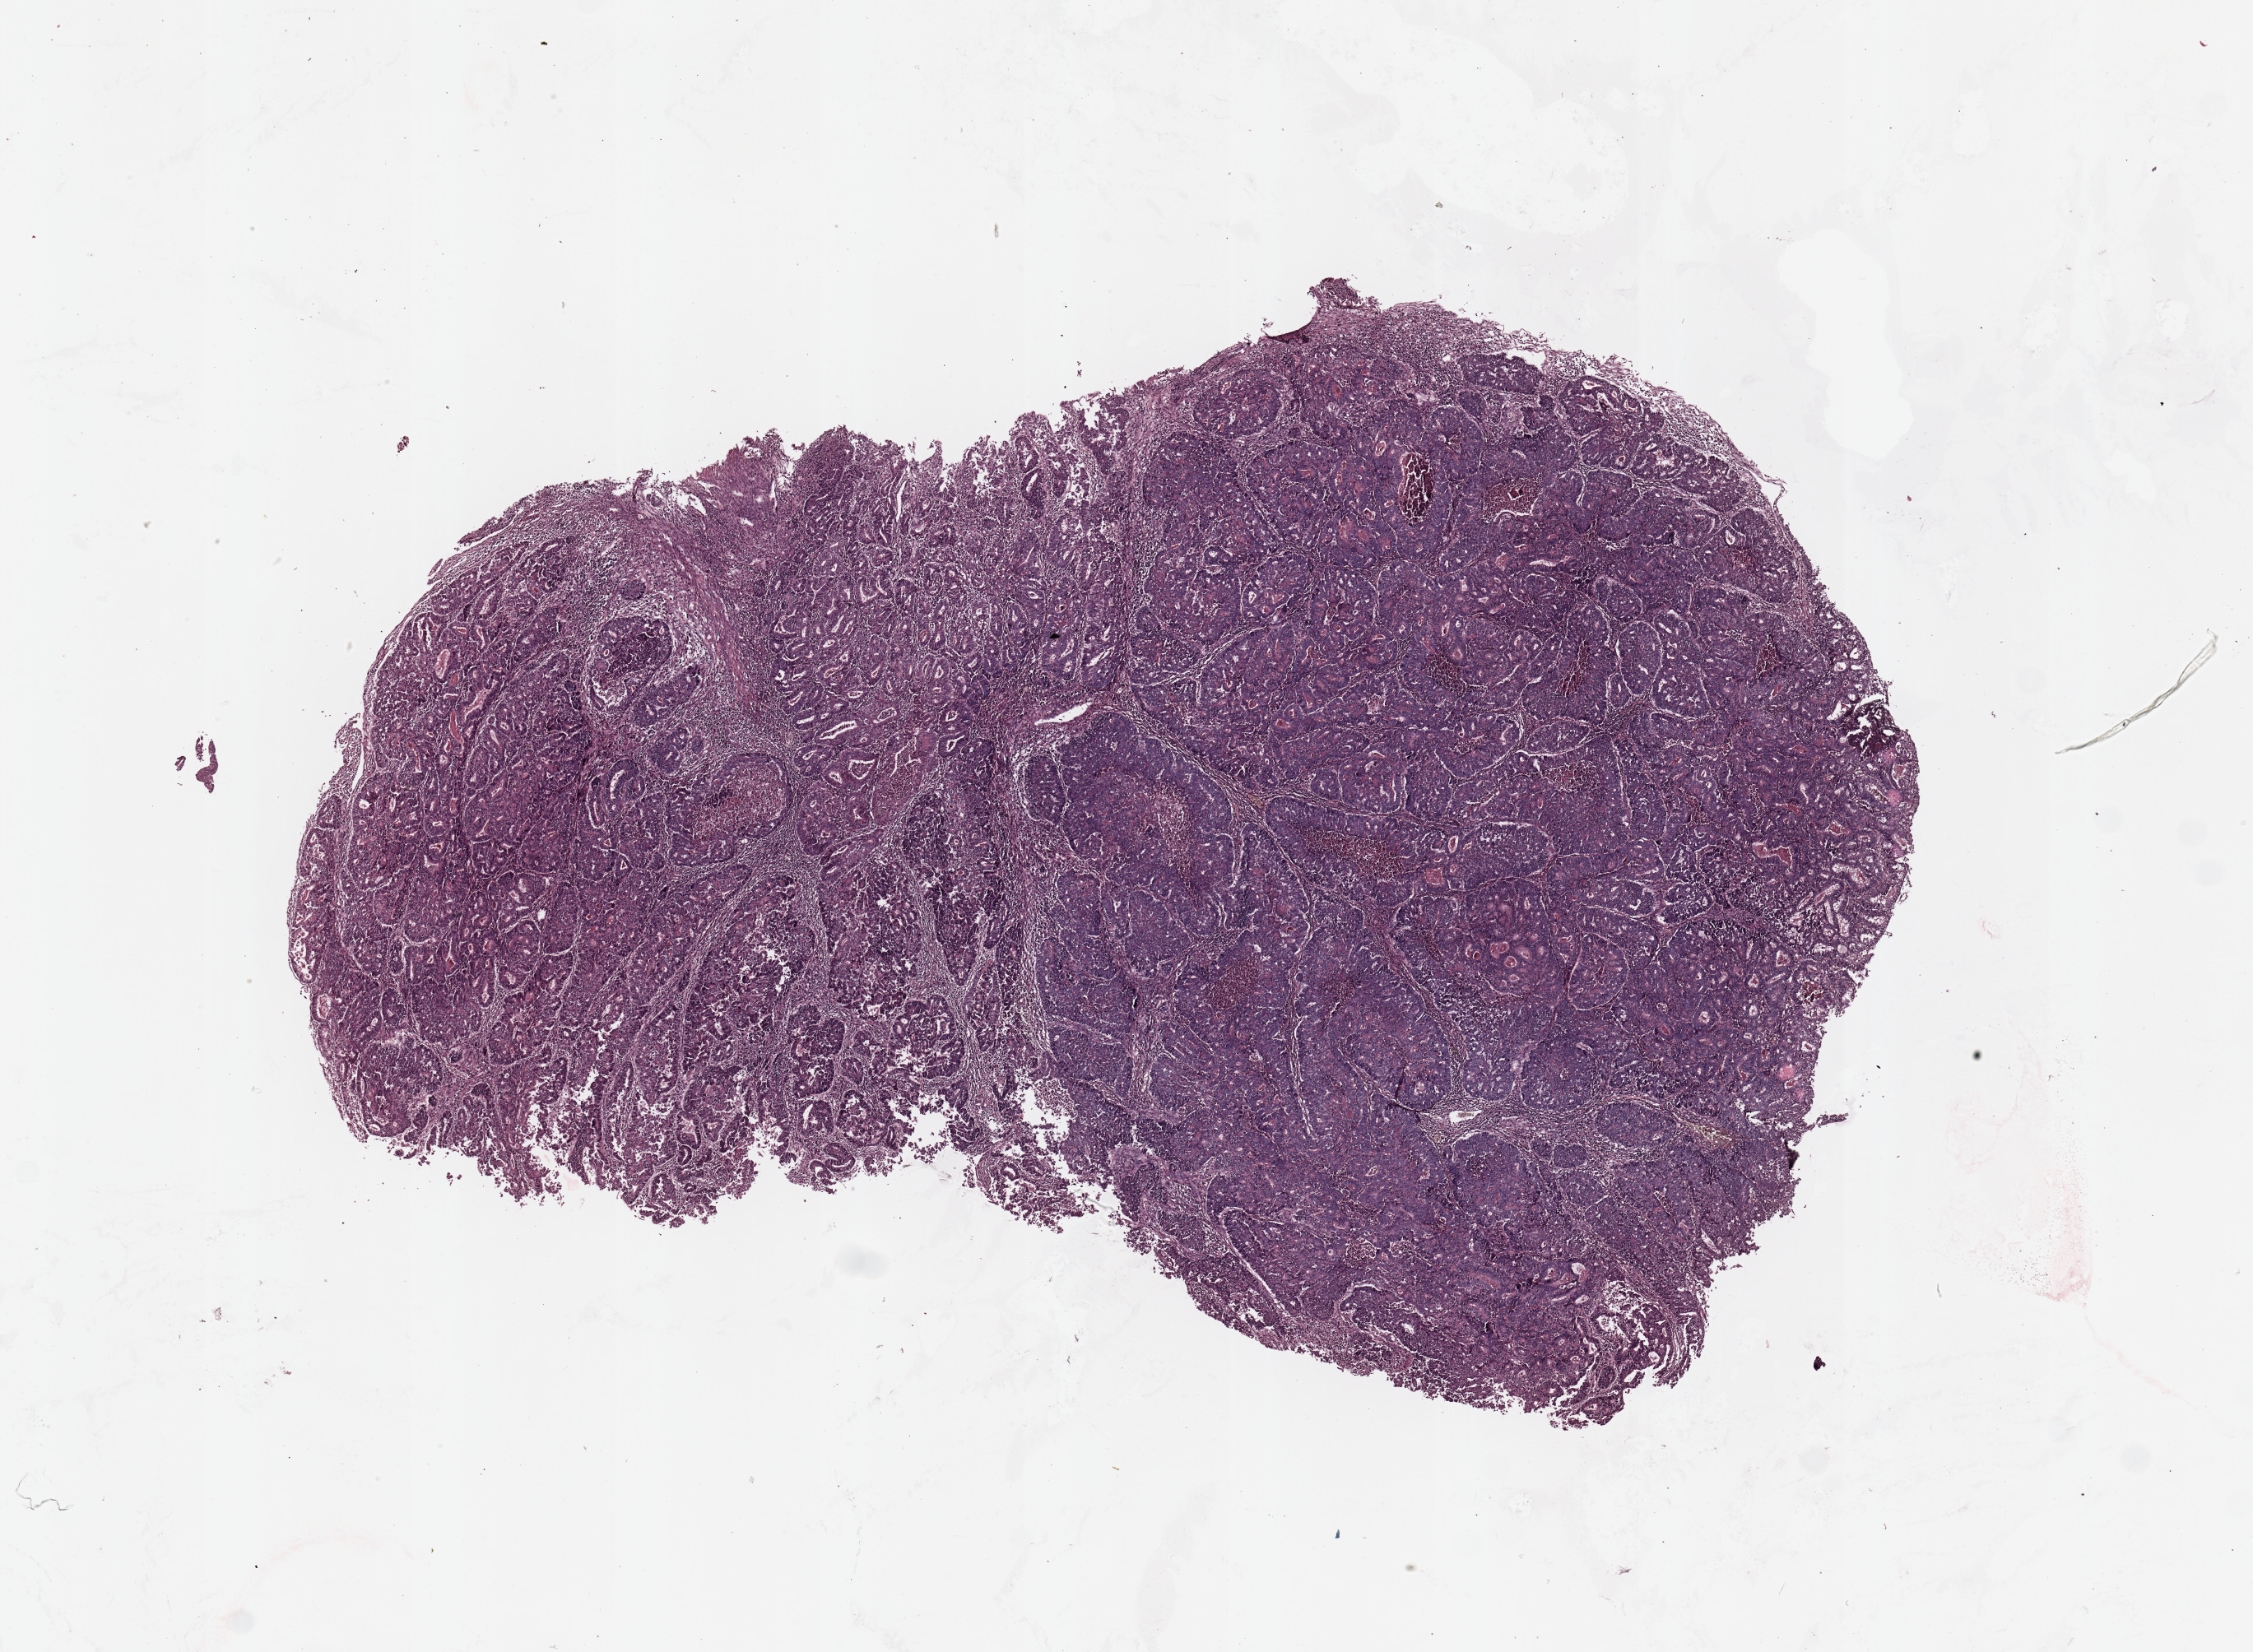
Hematoxylin and eosin (H&E) stained whole-slide image — whole scanned area (about 10.8 x 7.9 mm, slide scanned at 20x) shown as a low-resolution overview; tumour tissue sample, sampled site: uterus. Patient: female, age 69 years. Histologic grade: G2 (moderately differentiated). Slide review estimates, as recorded: tumour nuclei 90%, necrosis 5%.
Diagnosis: Endometrioid adenocarcinoma, NOS. AJCC pathologic stage: I.